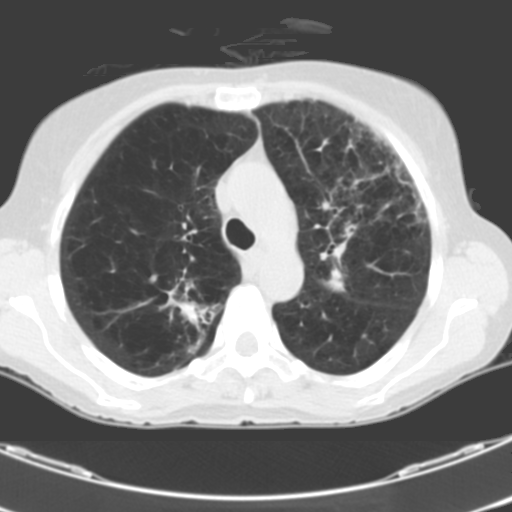
Low-dose screening chest CT, one axial slice. 120 kVp. One of 2 acquisitions stored at this slice position. Lung window (W 1500 / L -600 HU). 3.2 mm slice thickness. 512 × 512 image matrix, field of view 299 × 299 mm.
Annotated regions visible in this slice (manually delineated by an expert):
- lesion 1 (tumor): bounding box <325,276,345,291> (left, top, right, bottom; pixels)